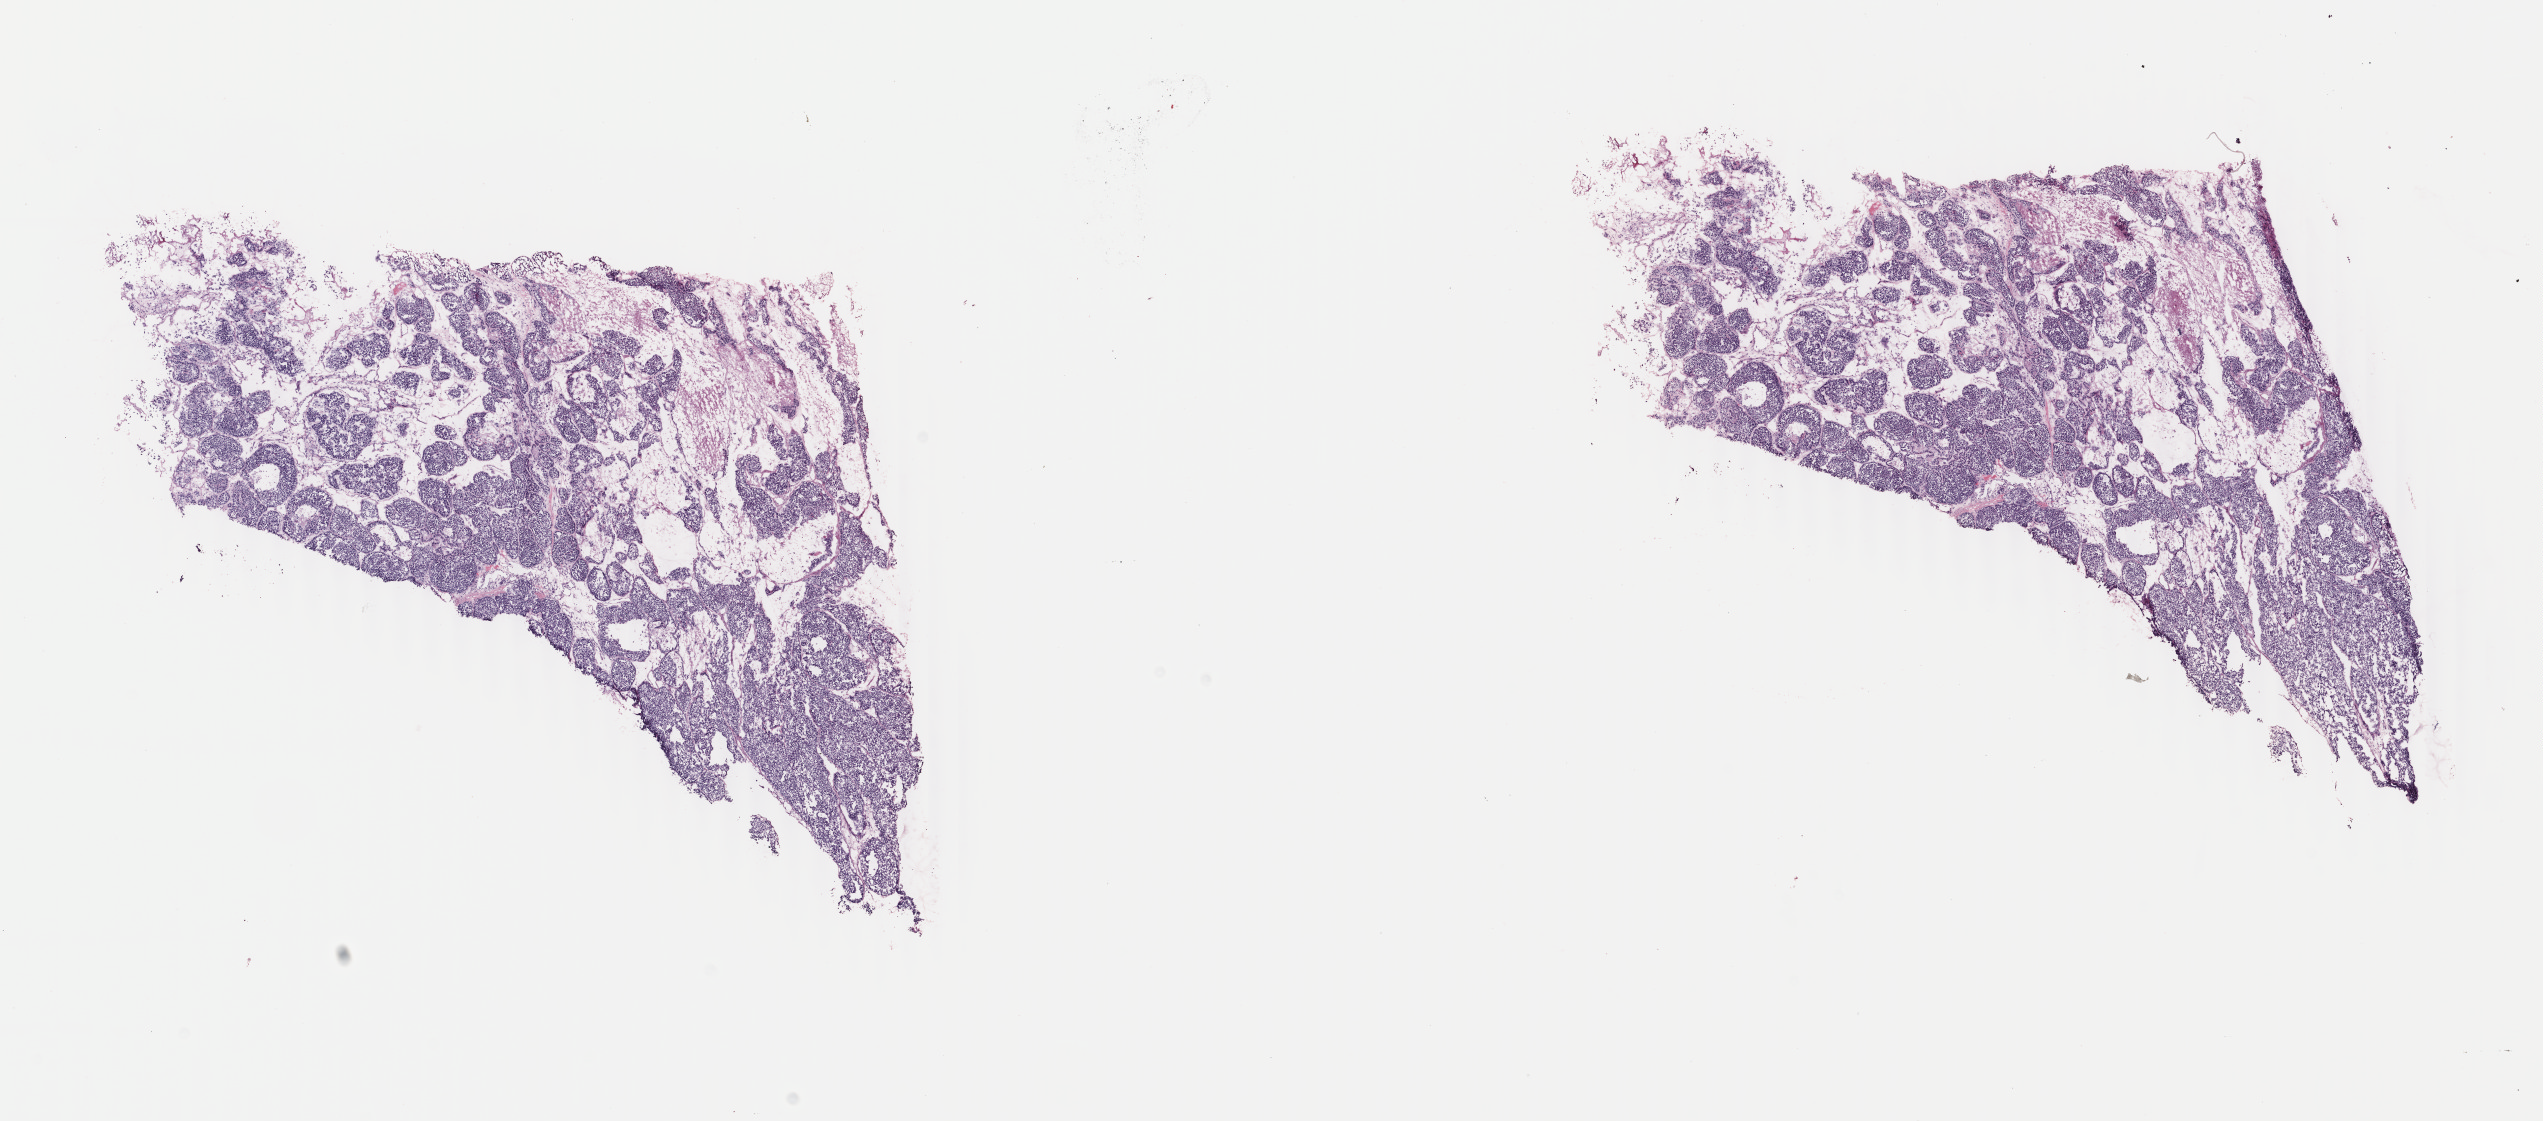
Whole-slide histology image, H&E — a low-resolution overview of the entire scanned area, about 20.2 x 8.9 mm; frozen section from the bottom of the tissue portion; breast, primary tumour sample. Patient: female, age at initial diagnosis 43 years. Slide review estimates, as recorded: tumour cells 80%, tumour nuclei 80%, normal cells 0%, stromal cells 10%, necrosis 10%. Infiltration values recorded for this section: lymphocyte infiltration 0%, monocyte infiltration 0%, neutrophil infiltration 0%.
• laterality: left
• AJCC pathologic stage: IIA (6th edition)
• histologic diagnosis: Infiltrating duct carcinoma, NOS
• lymph nodes positive (case pathology): 0 of 5 examined